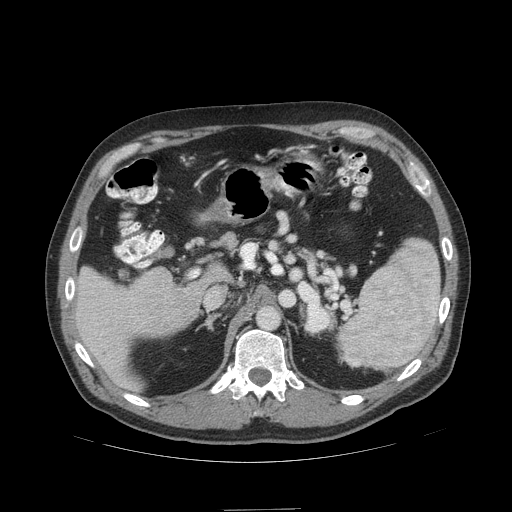
Contrast-enhanced abdominal CT (liver protocol), one axial slice. Position 63 of 99 along the scan axis. Reconstruction kernel STANDARD. 140 kVp. Soft-tissue window (W 400 / L 40 HU). 2.5 mm slice thickness. 512 × 512 image matrix, field of view 440 × 440 mm. Case-level facts recorded for this patient, not image findings: diagnosis: hepatocellular carcinoma (patient treated with transarterial chemoembolisation; whether this scan precedes or follows treatment is not stated here); TNM stage (as recorded): Stage-I; Child-Pugh class: A; tumour nodularity: uninodular; tumour size: 3.6 cm.
Annotated regions visible in this slice (semi-automatic segmentation, software-assisted and operator-edited):
- liver parenchyma outside the tumour (the mass and vessels are separate outlines, so this box may not span the whole liver): bounding box (x1, y1, x2, y2) in pixels: (72, 266, 198, 390)